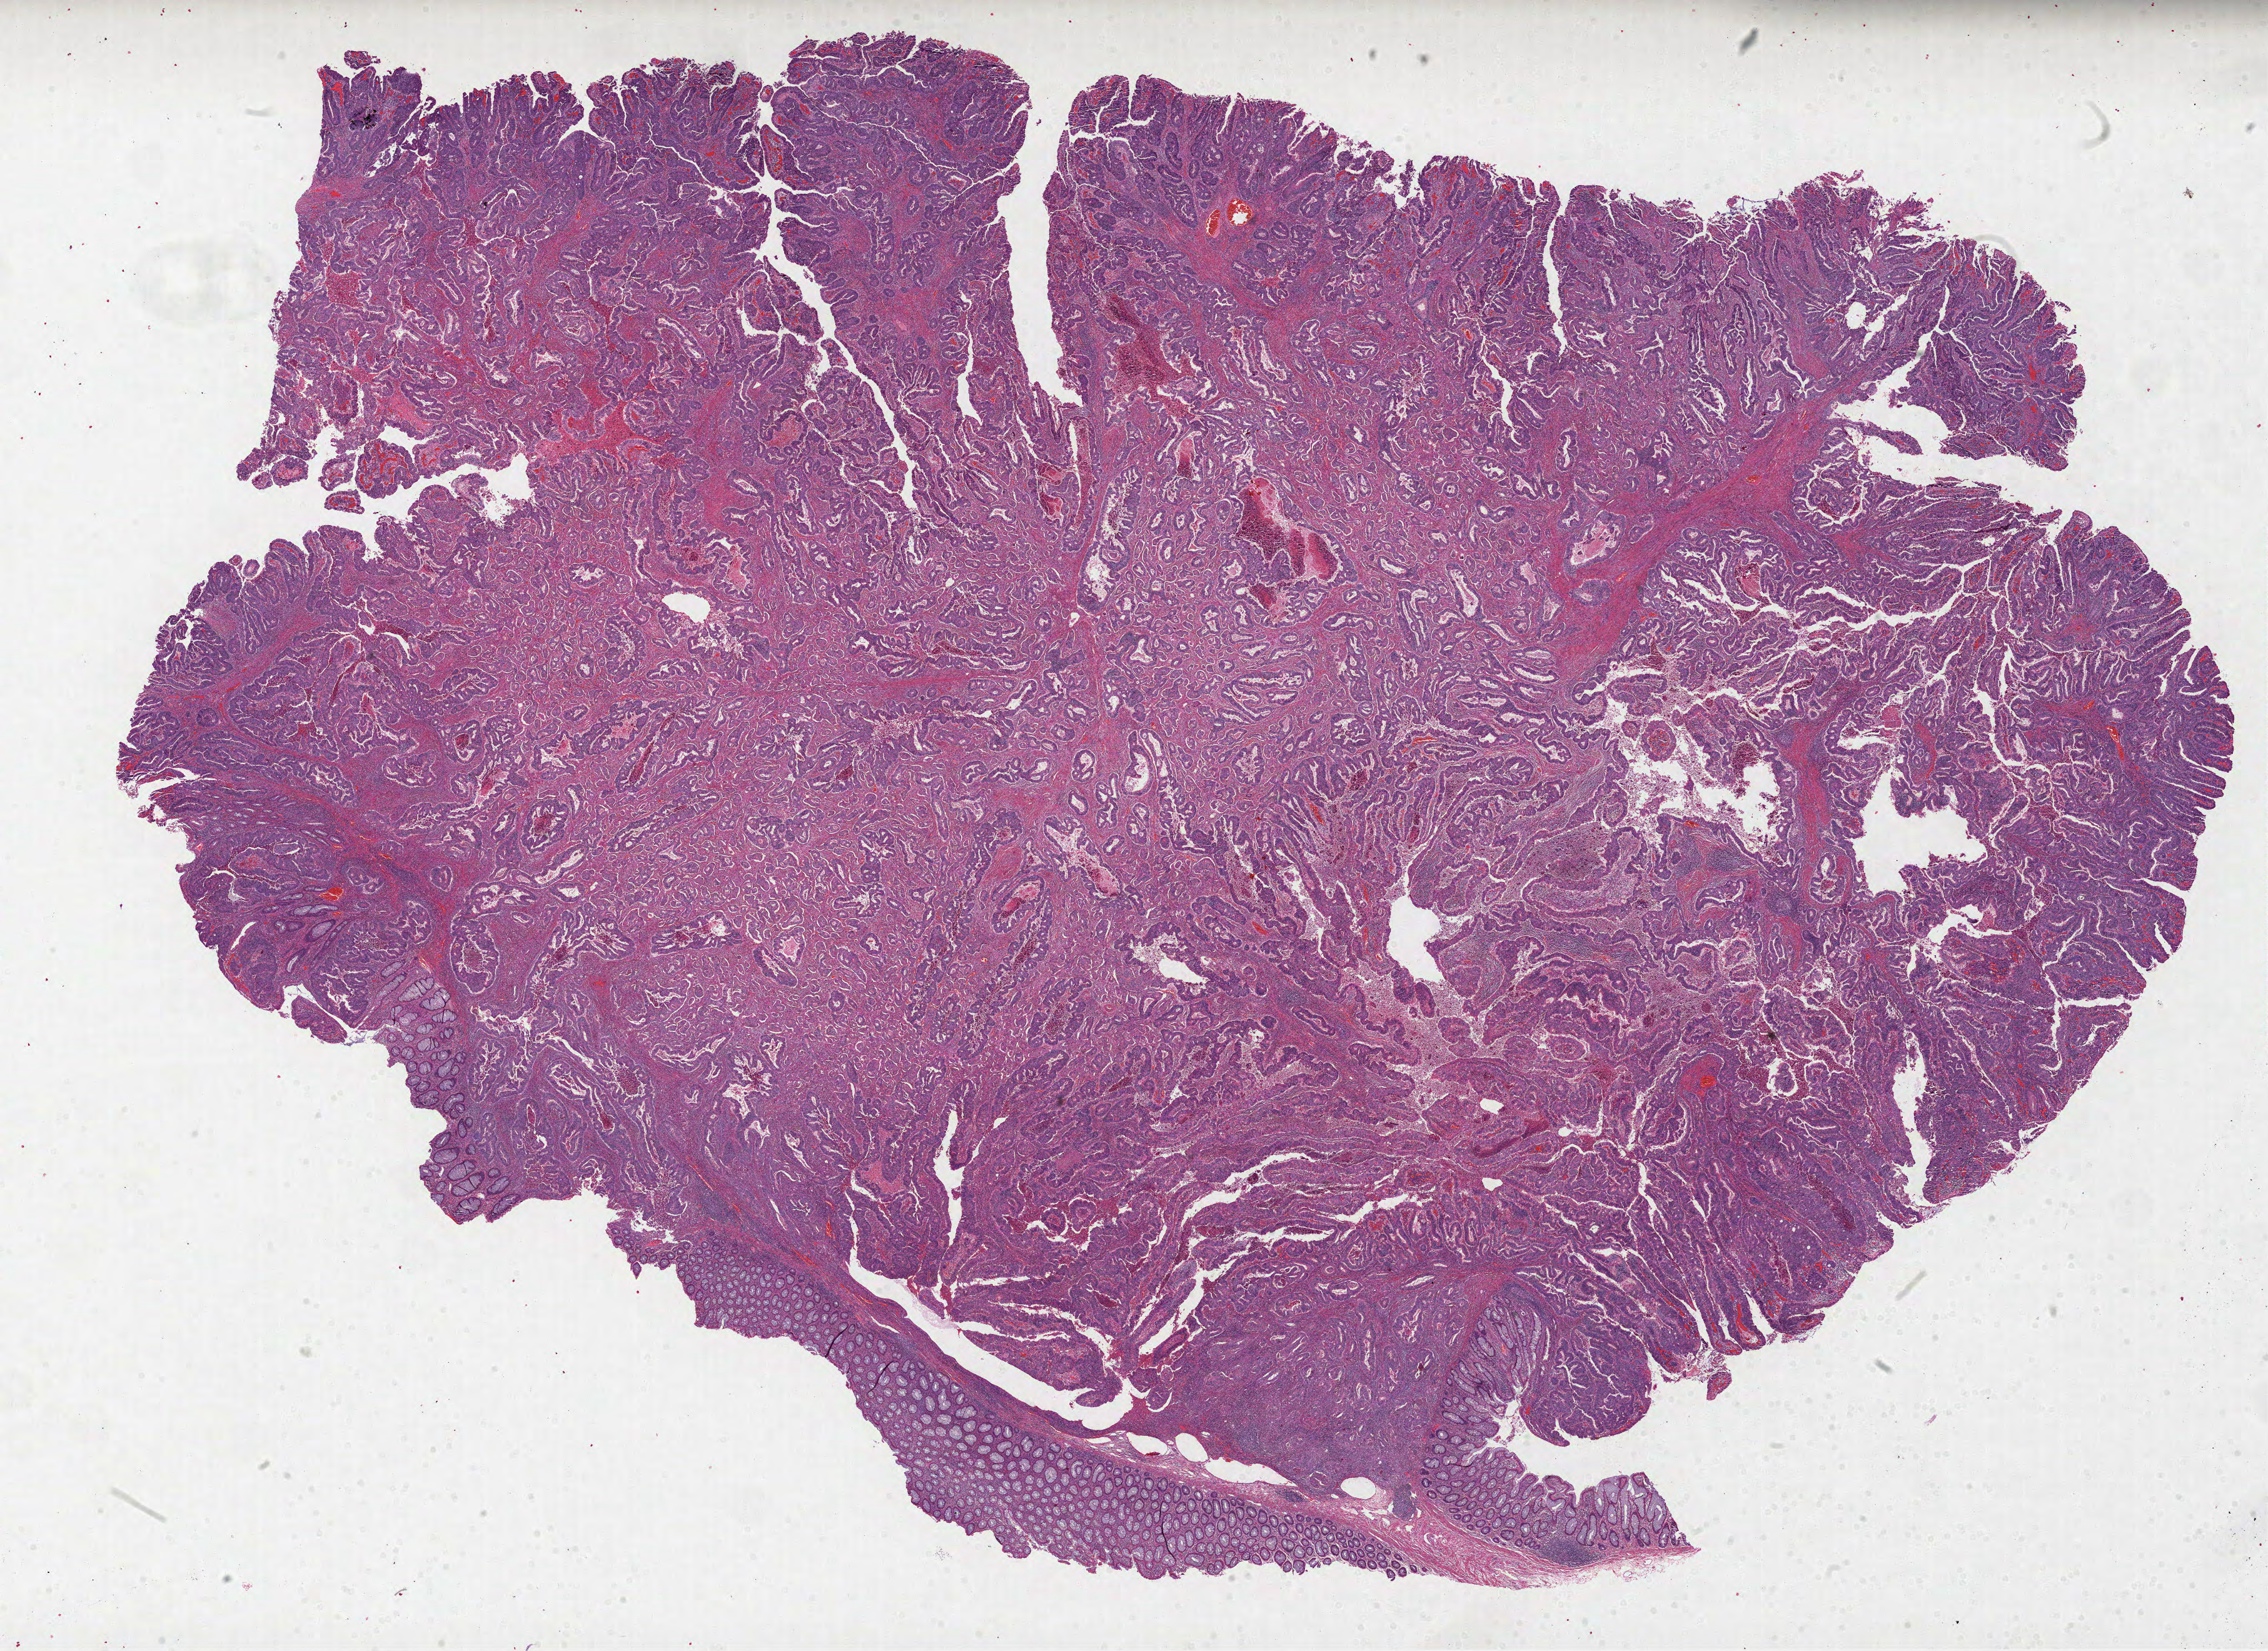
H&E-stained whole-slide image — a low-resolution overview of the entire scanned area, about 29.2 x 21.3 mm. Formalin-fixed paraffin-embedded (FFPE) diagnostic section. Primary tumour sample from the colon. Female, age 34 years at initial diagnosis.
Histologic diagnosis: Adenocarcinoma, NOS (rectosigmoid junction).